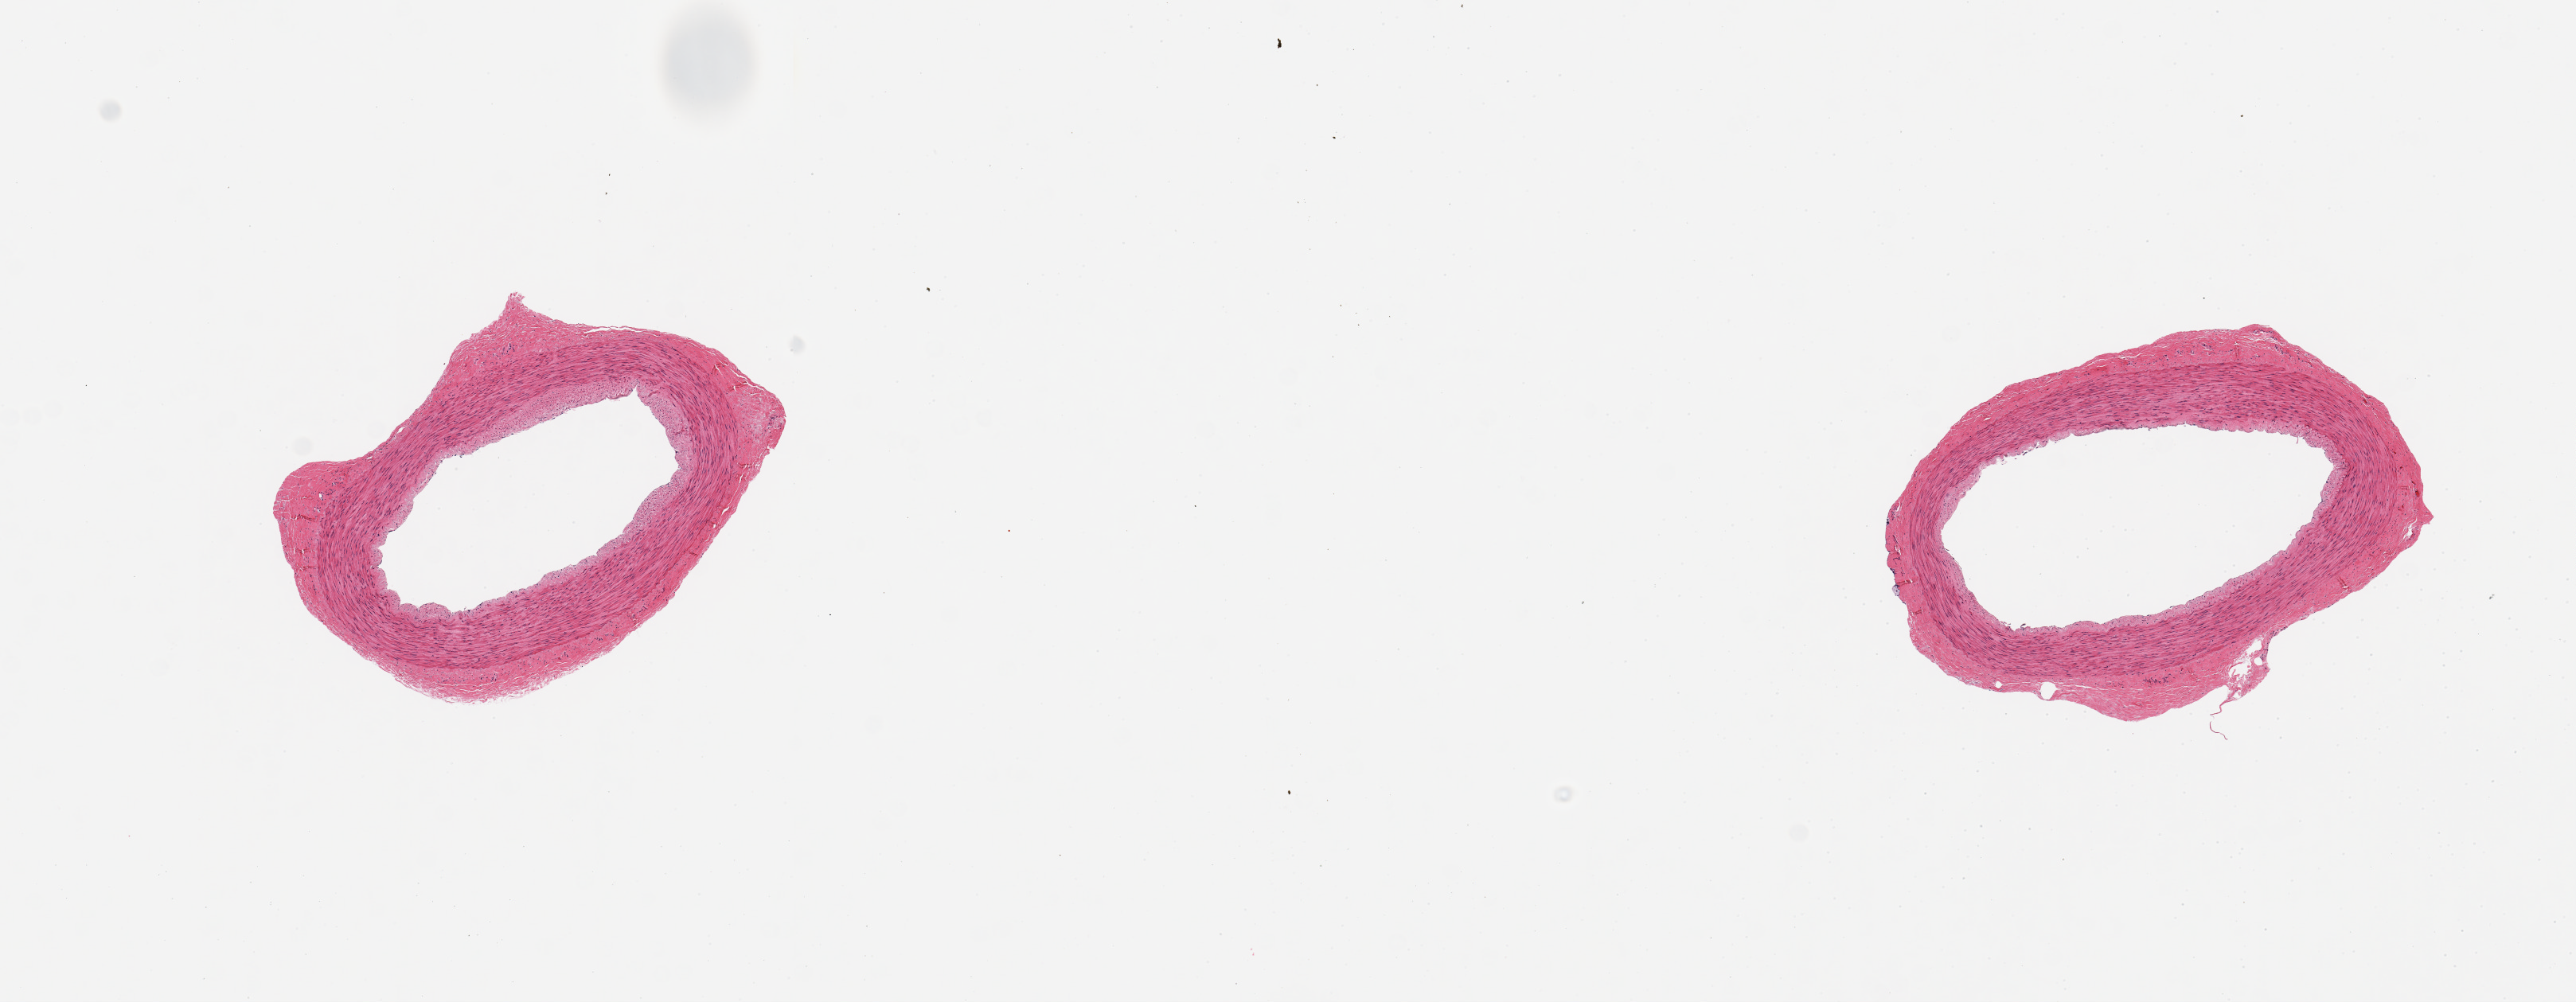
Whole-slide image, haematoxylin and eosin stain — a low-resolution overview of the entire scanned area, about 12.8 x 5.0 mm; PAXgene-fixed paraffin-embedded (PFPE) section; sampled site (target tissue): tibial artery; donor tissue sample.
Reviewer comment on this tissue sample: 2 pieces; patent lumen; up to 0.3 mm adventitia.